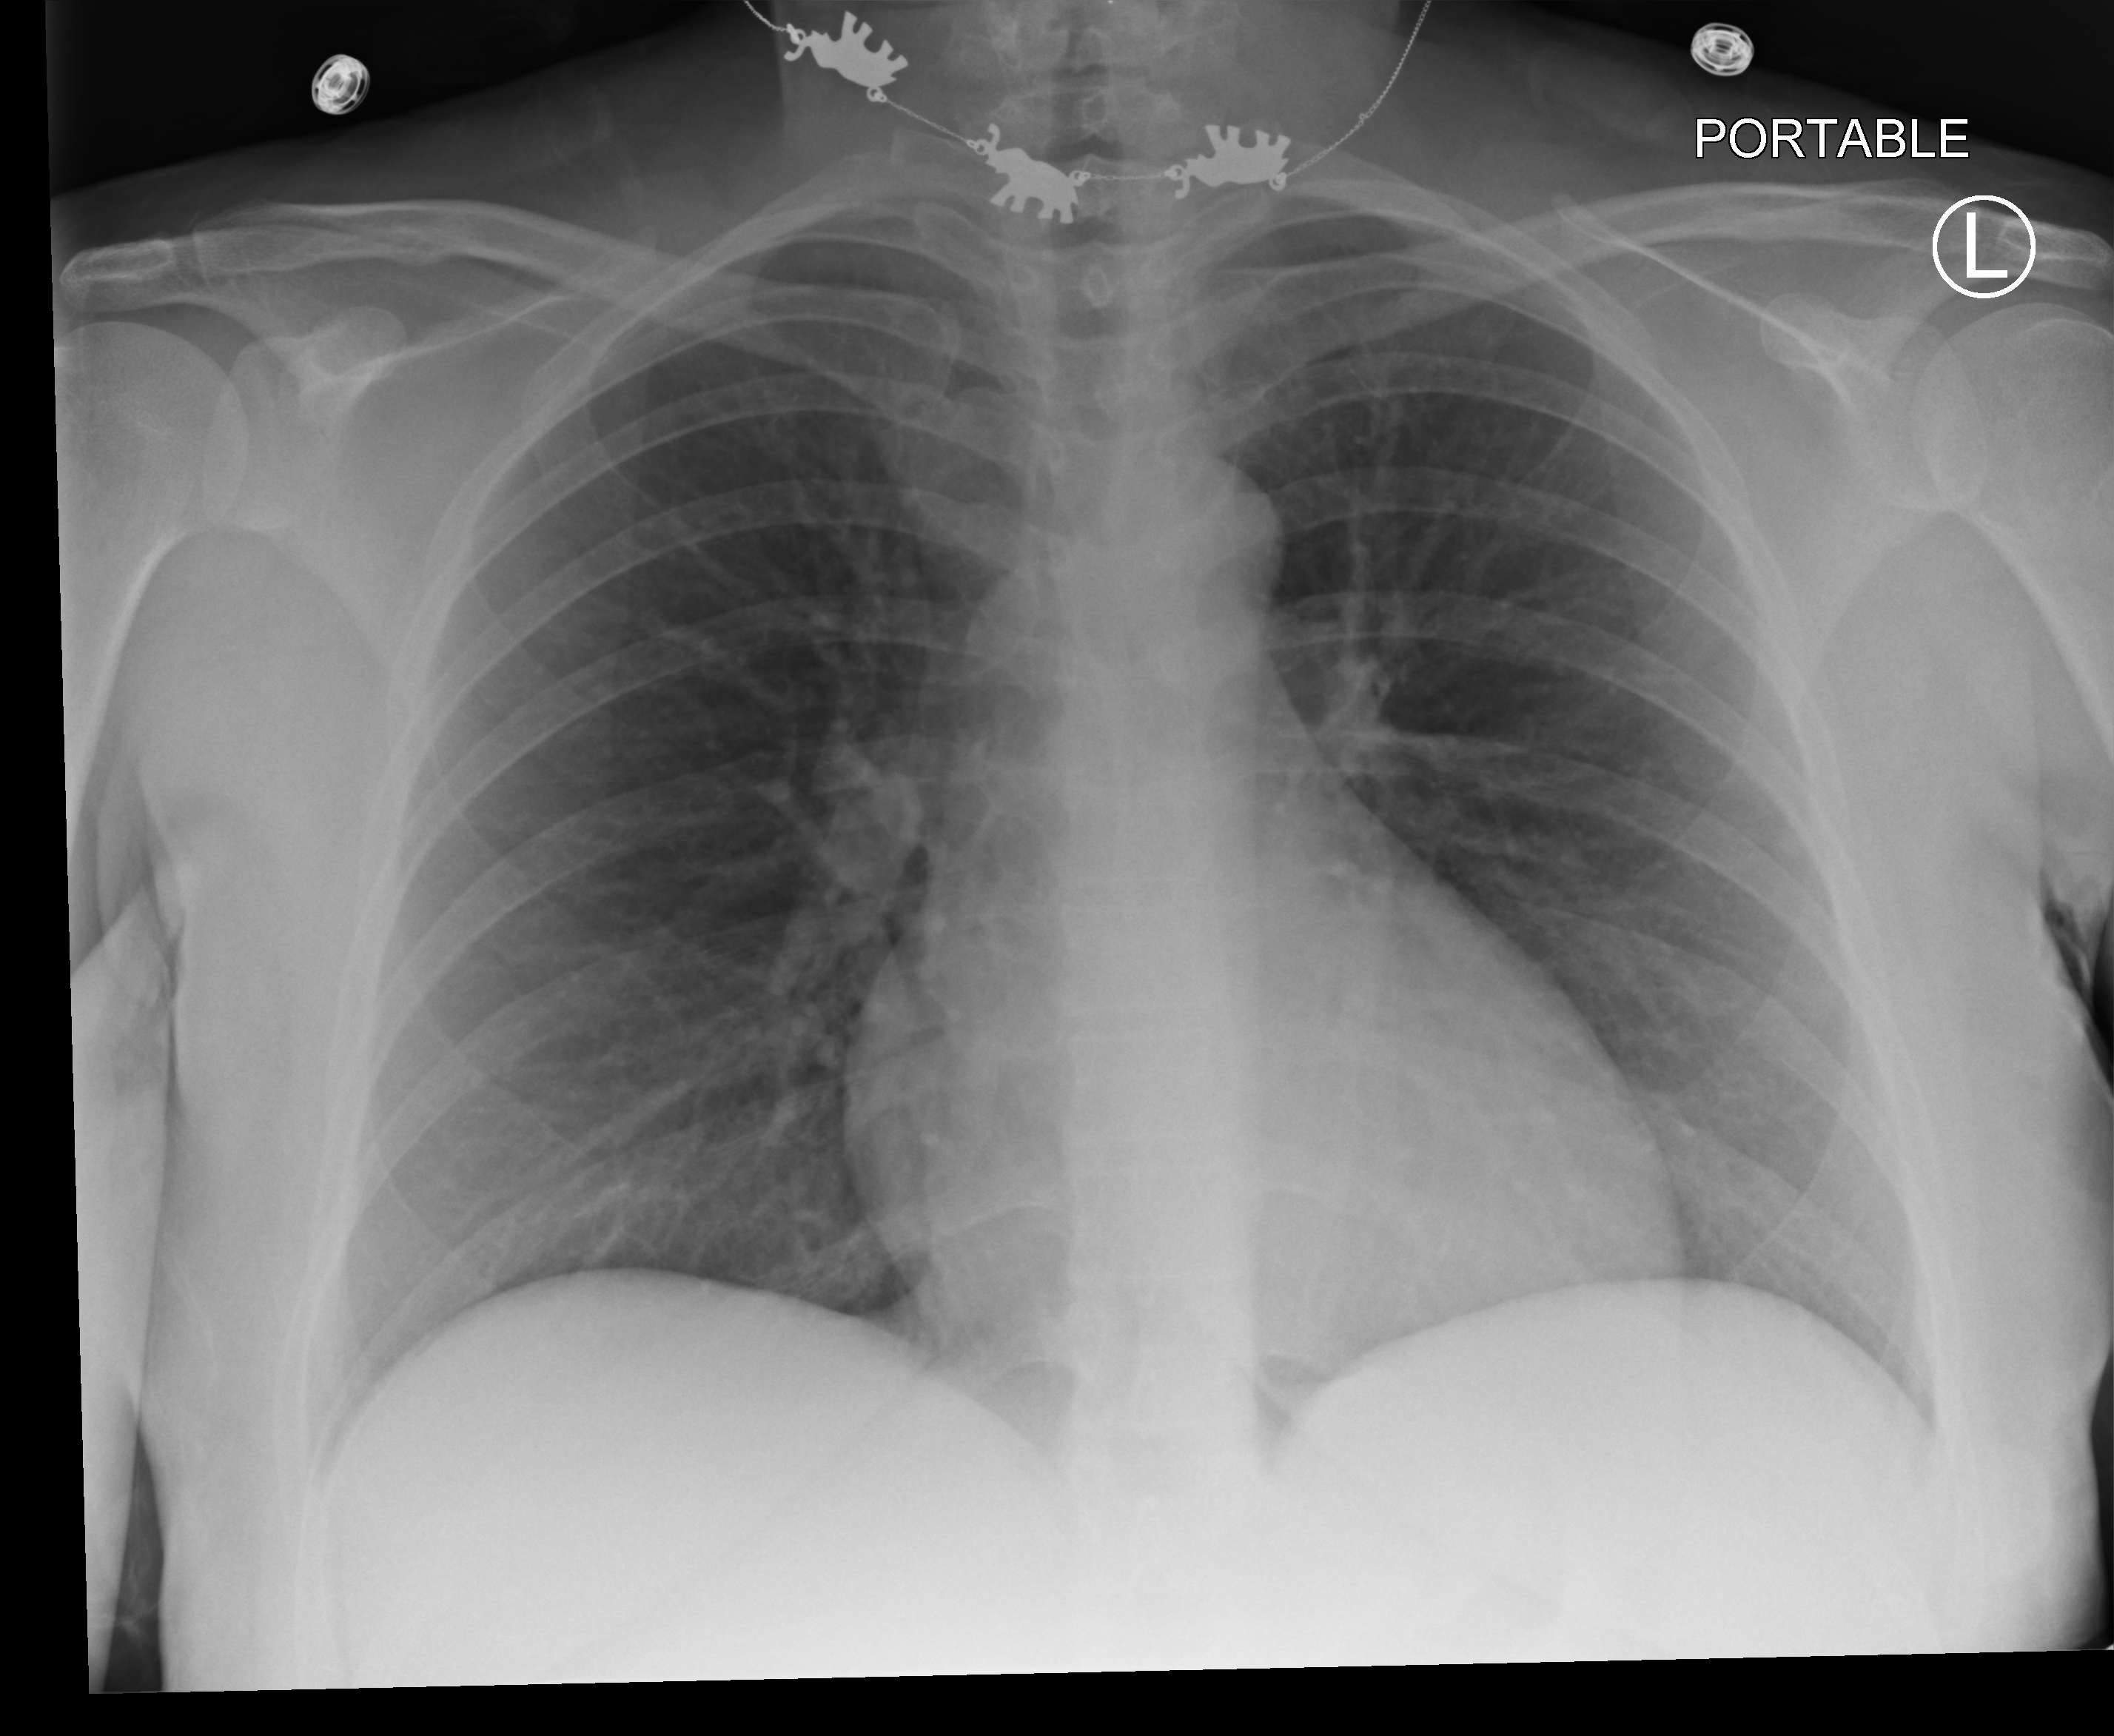
Portable chest radiograph; anteroposterior (AP) projection. Female patient hospitalised with COVID-19, age 18–59 years.
Hospital-stay facts (about this admission, not read from this image; timing relative to this image not recorded): diabetes (admission record): no.